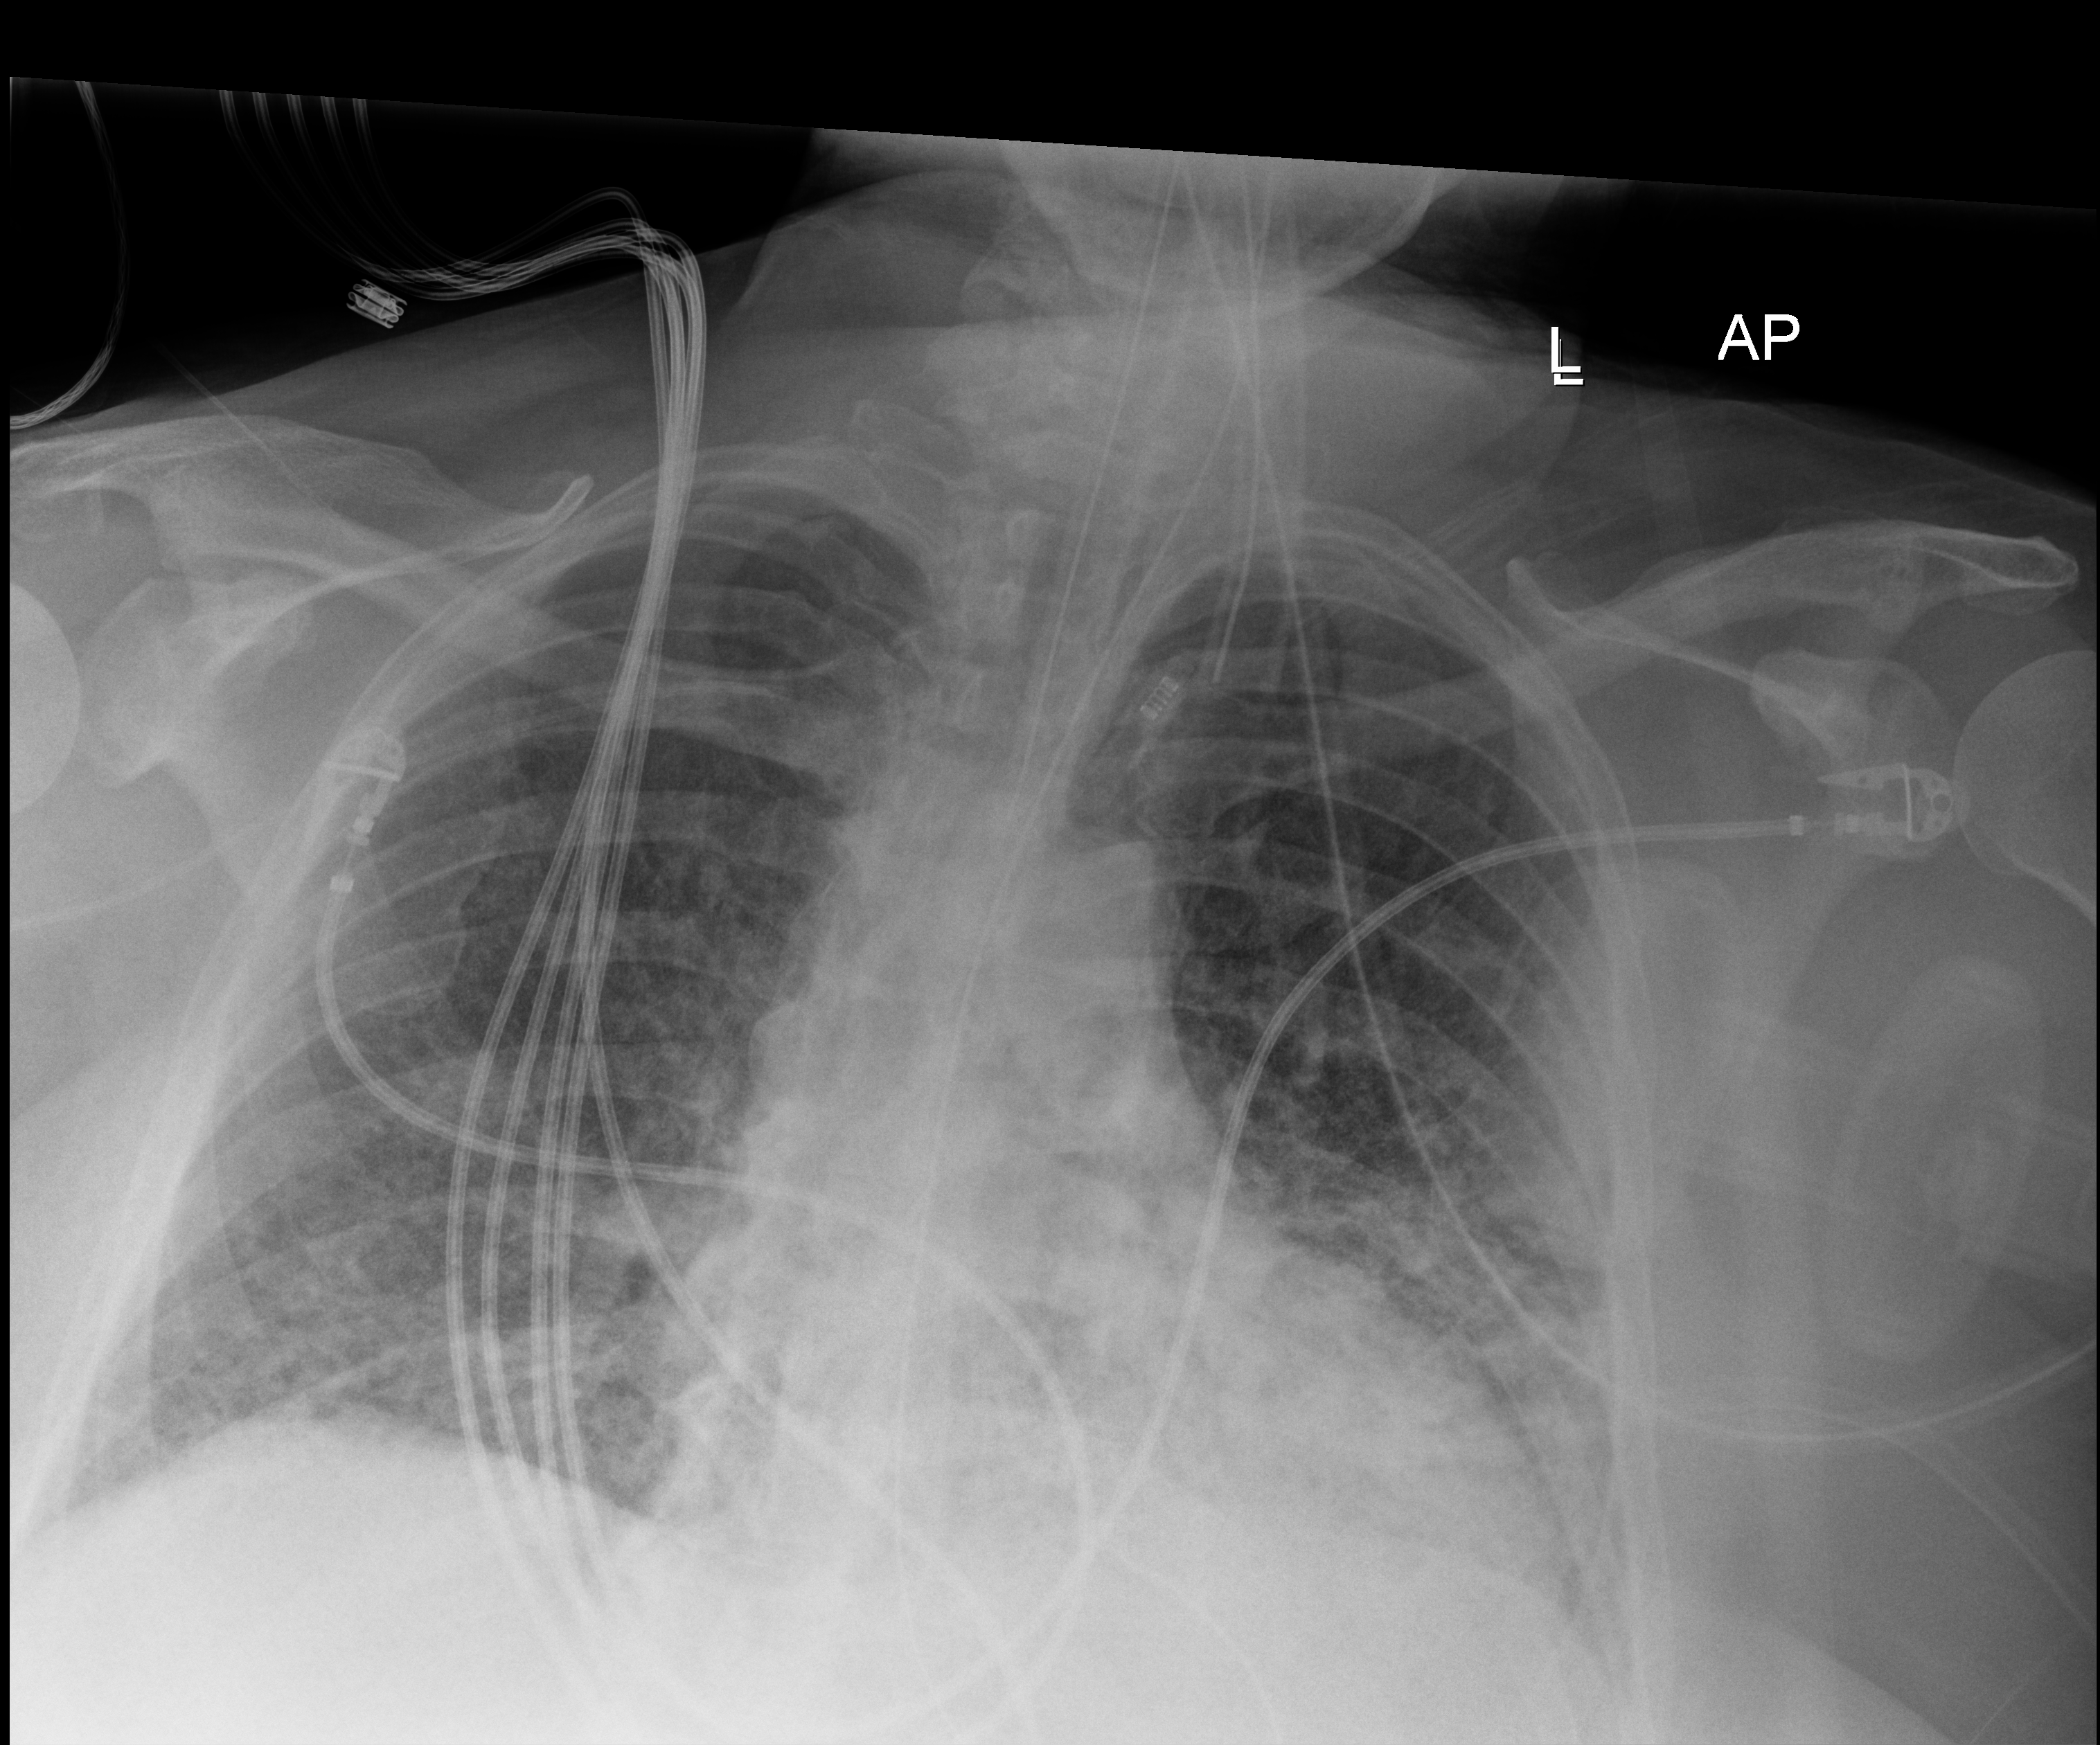
Chest radiograph; anteroposterior (AP) projection. Adult patient hospitalised with COVID-19, age 18–59 years.
Hospital-stay facts (about this admission, not read from this image; timing relative to this image not recorded):
- admitted to intensive care during this hospital stay: yes
- length of hospital stay: 28 days